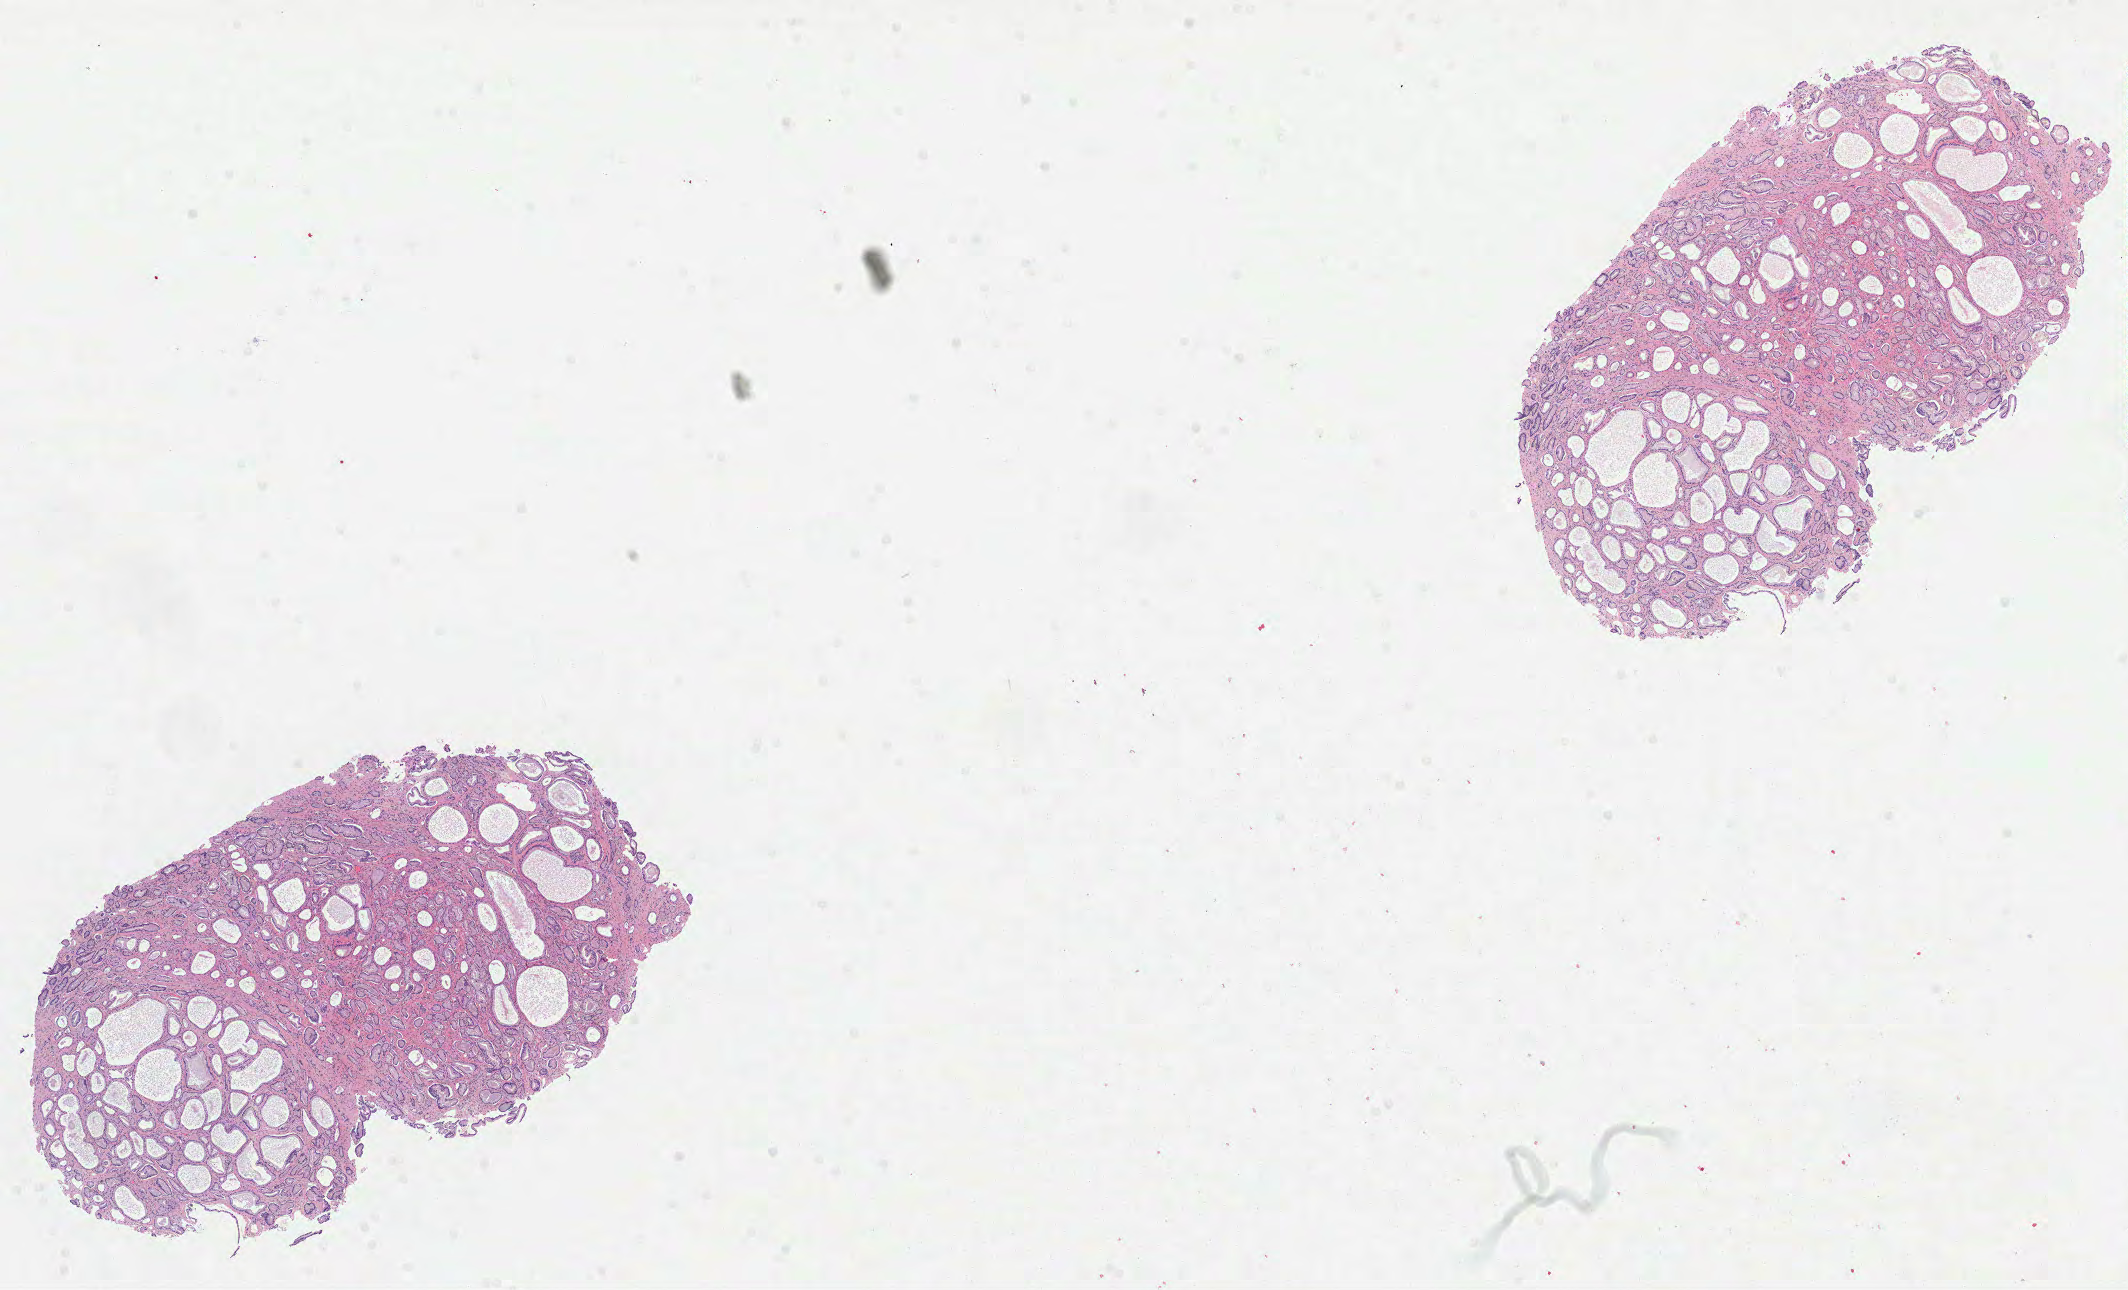
Digitized Hematoxylin and eosin (H&E) stained tissue section (whole slide) — a low-resolution overview of the entire scanned area, about 17.2 x 10.4 mm. FFPE section. Prostate, primary tumour sample. Patient: male, age at initial diagnosis 68 years. Gleason score: 7 (3+4).
Histologic diagnosis: Acinar cell carcinoma. Laterality: right.